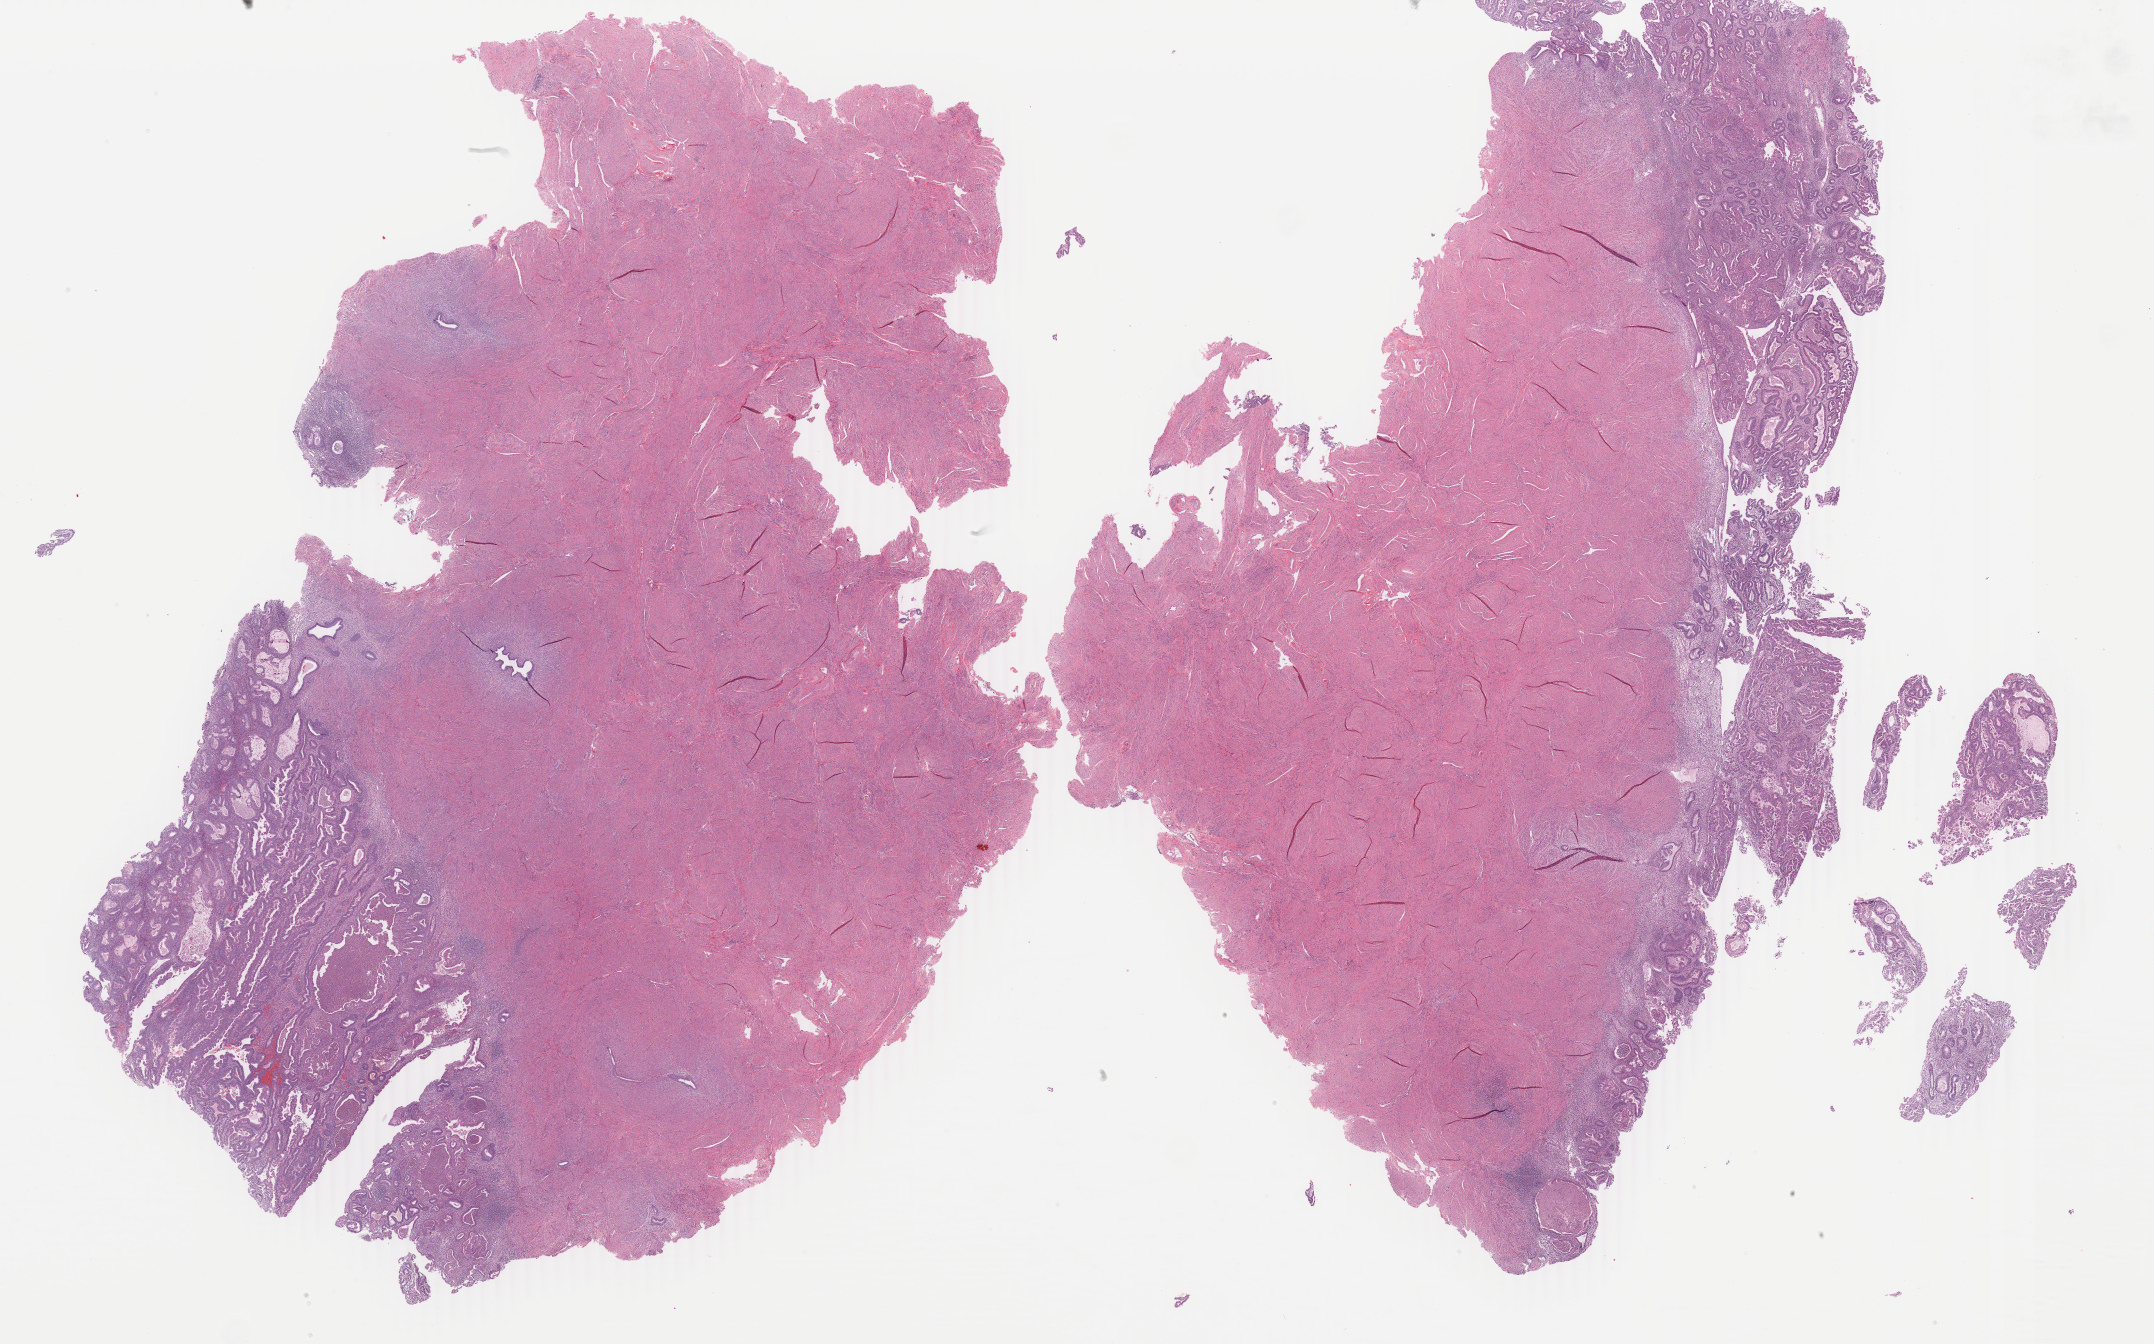
Whole-slide histology image, Hematoxylin and eosin (H&E) stained, whole scanned area (about 34.3 x 21.4 mm) shown as a low-resolution overview; FFPE section; primary tumour sample from the uterus. Female, age 54 years at initial diagnosis. Histologic grade: G2 (moderately differentiated).
- pathologic diagnosis: Endometrioid adenocarcinoma, NOS (endometrium)
- FIGO stage: IA